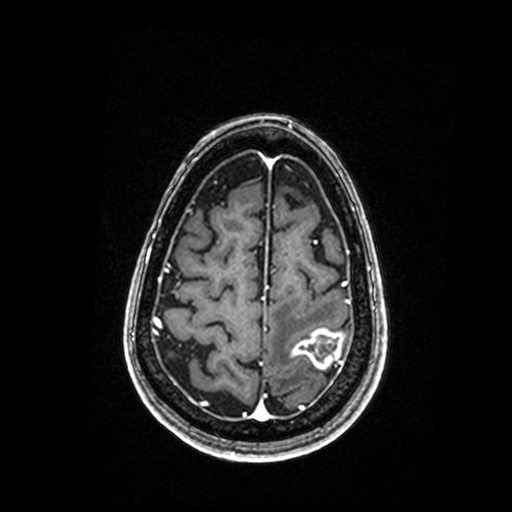
Brain MRI from a brain-tumour surgery series, one axial slice. Slice 48 of 192 in the series (ordered by position). T1-weighted post-contrast. 512 × 512 image matrix, field of view 250 × 250 mm. From the clinical record (not read from this slice): histopathology: Metastastic Carcinoma, Poorly Differentiated; tumour location: Left Parietal.
Structures marked on this image (manually delineated by an expert):
- tumour: box from (x=292, y=329) to (x=343, y=369) px